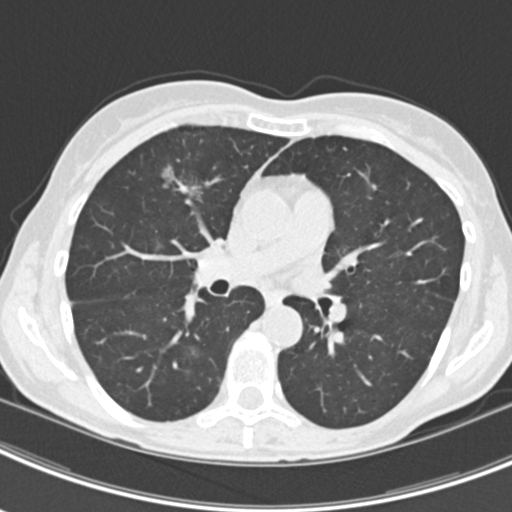
Chest CT (low-dose screening protocol), one axial image; second annual screen; lung window (W 1500 / L -600 HU); 2 mm slice thickness; standard (soft-tissue) reconstruction kernel (B30f). Female participant, aged 63 years at enrolment. Current smoker at enrolment.
Lesion marked by an expert reader, bounding box [x1, y1, x2, y2] px = [159, 156, 219, 209]. The screening reader recorded 9 non-calcified nodules or masses ≥4 mm on this exam; which of them this box marks is not recorded. Later outcome: lung cancer diagnosed 408 days after this screen — bronchiolo-alveolar adenocarcinoma, NOS, right upper lobe, right middle lobe, right lower lobe, left upper lobe, left lower lobe, moderately differentiated (G2), stage IV (AJCC 6th edition).